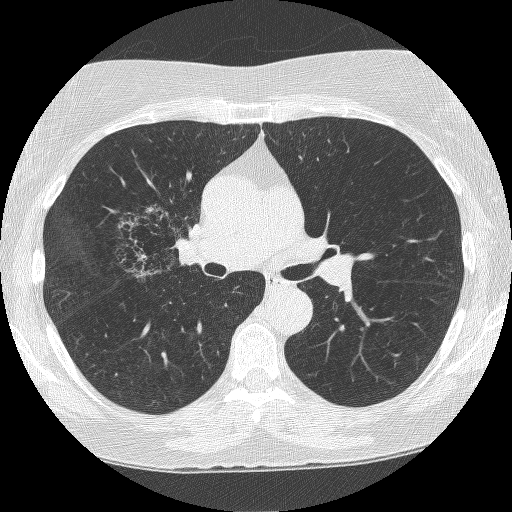
Chest CT (low-dose screening protocol), one axial image; second annual screen; lung window (W 1500 / L -600 HU); 120 kVp; 512 × 512 image matrix. Female, age 64 years at enrolment.
• Lesion marked by an expert reader, bounding box <116,205,203,288> (left, top, right, bottom; pixels).
• The screening reader recorded 4 non-calcified nodules or masses ≥4 mm on this exam (right upper lobe, right upper lobe, right upper lobe, left upper lobe); which of them this box marks is not recorded.
• Official screen result: positive, other.
• Participant outcome: lung cancer diagnosed 381 days after this screen (after the third annual screen) — adenocarcinoma, NOS, right upper lobe, right middle lobe, right hilum, stage IV (AJCC 6th edition), 85 mm at pathology.